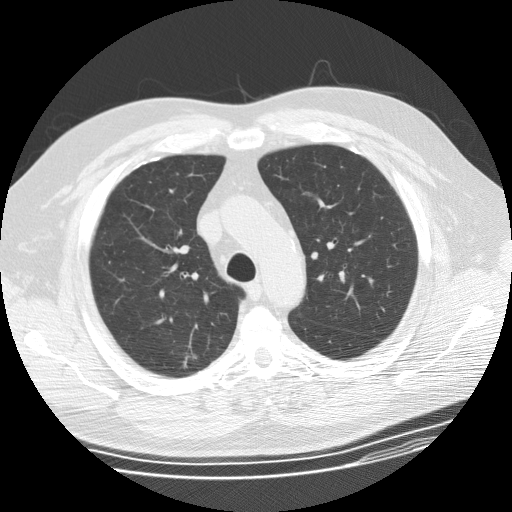
Low-dose screening chest CT, one axial slice; position 112 of 155 along the scan axis; reconstruction kernel STANDARD; 120 kVp; lung window (W 1500 / L -600 HU); 2.5 mm slice thickness; 512 × 512 image matrix.
Structures marked on this image (expert manual segmentation):
- lesion 1 (tumor, upper lobe of right lung): box from (x=182, y=355) to (x=197, y=369) px